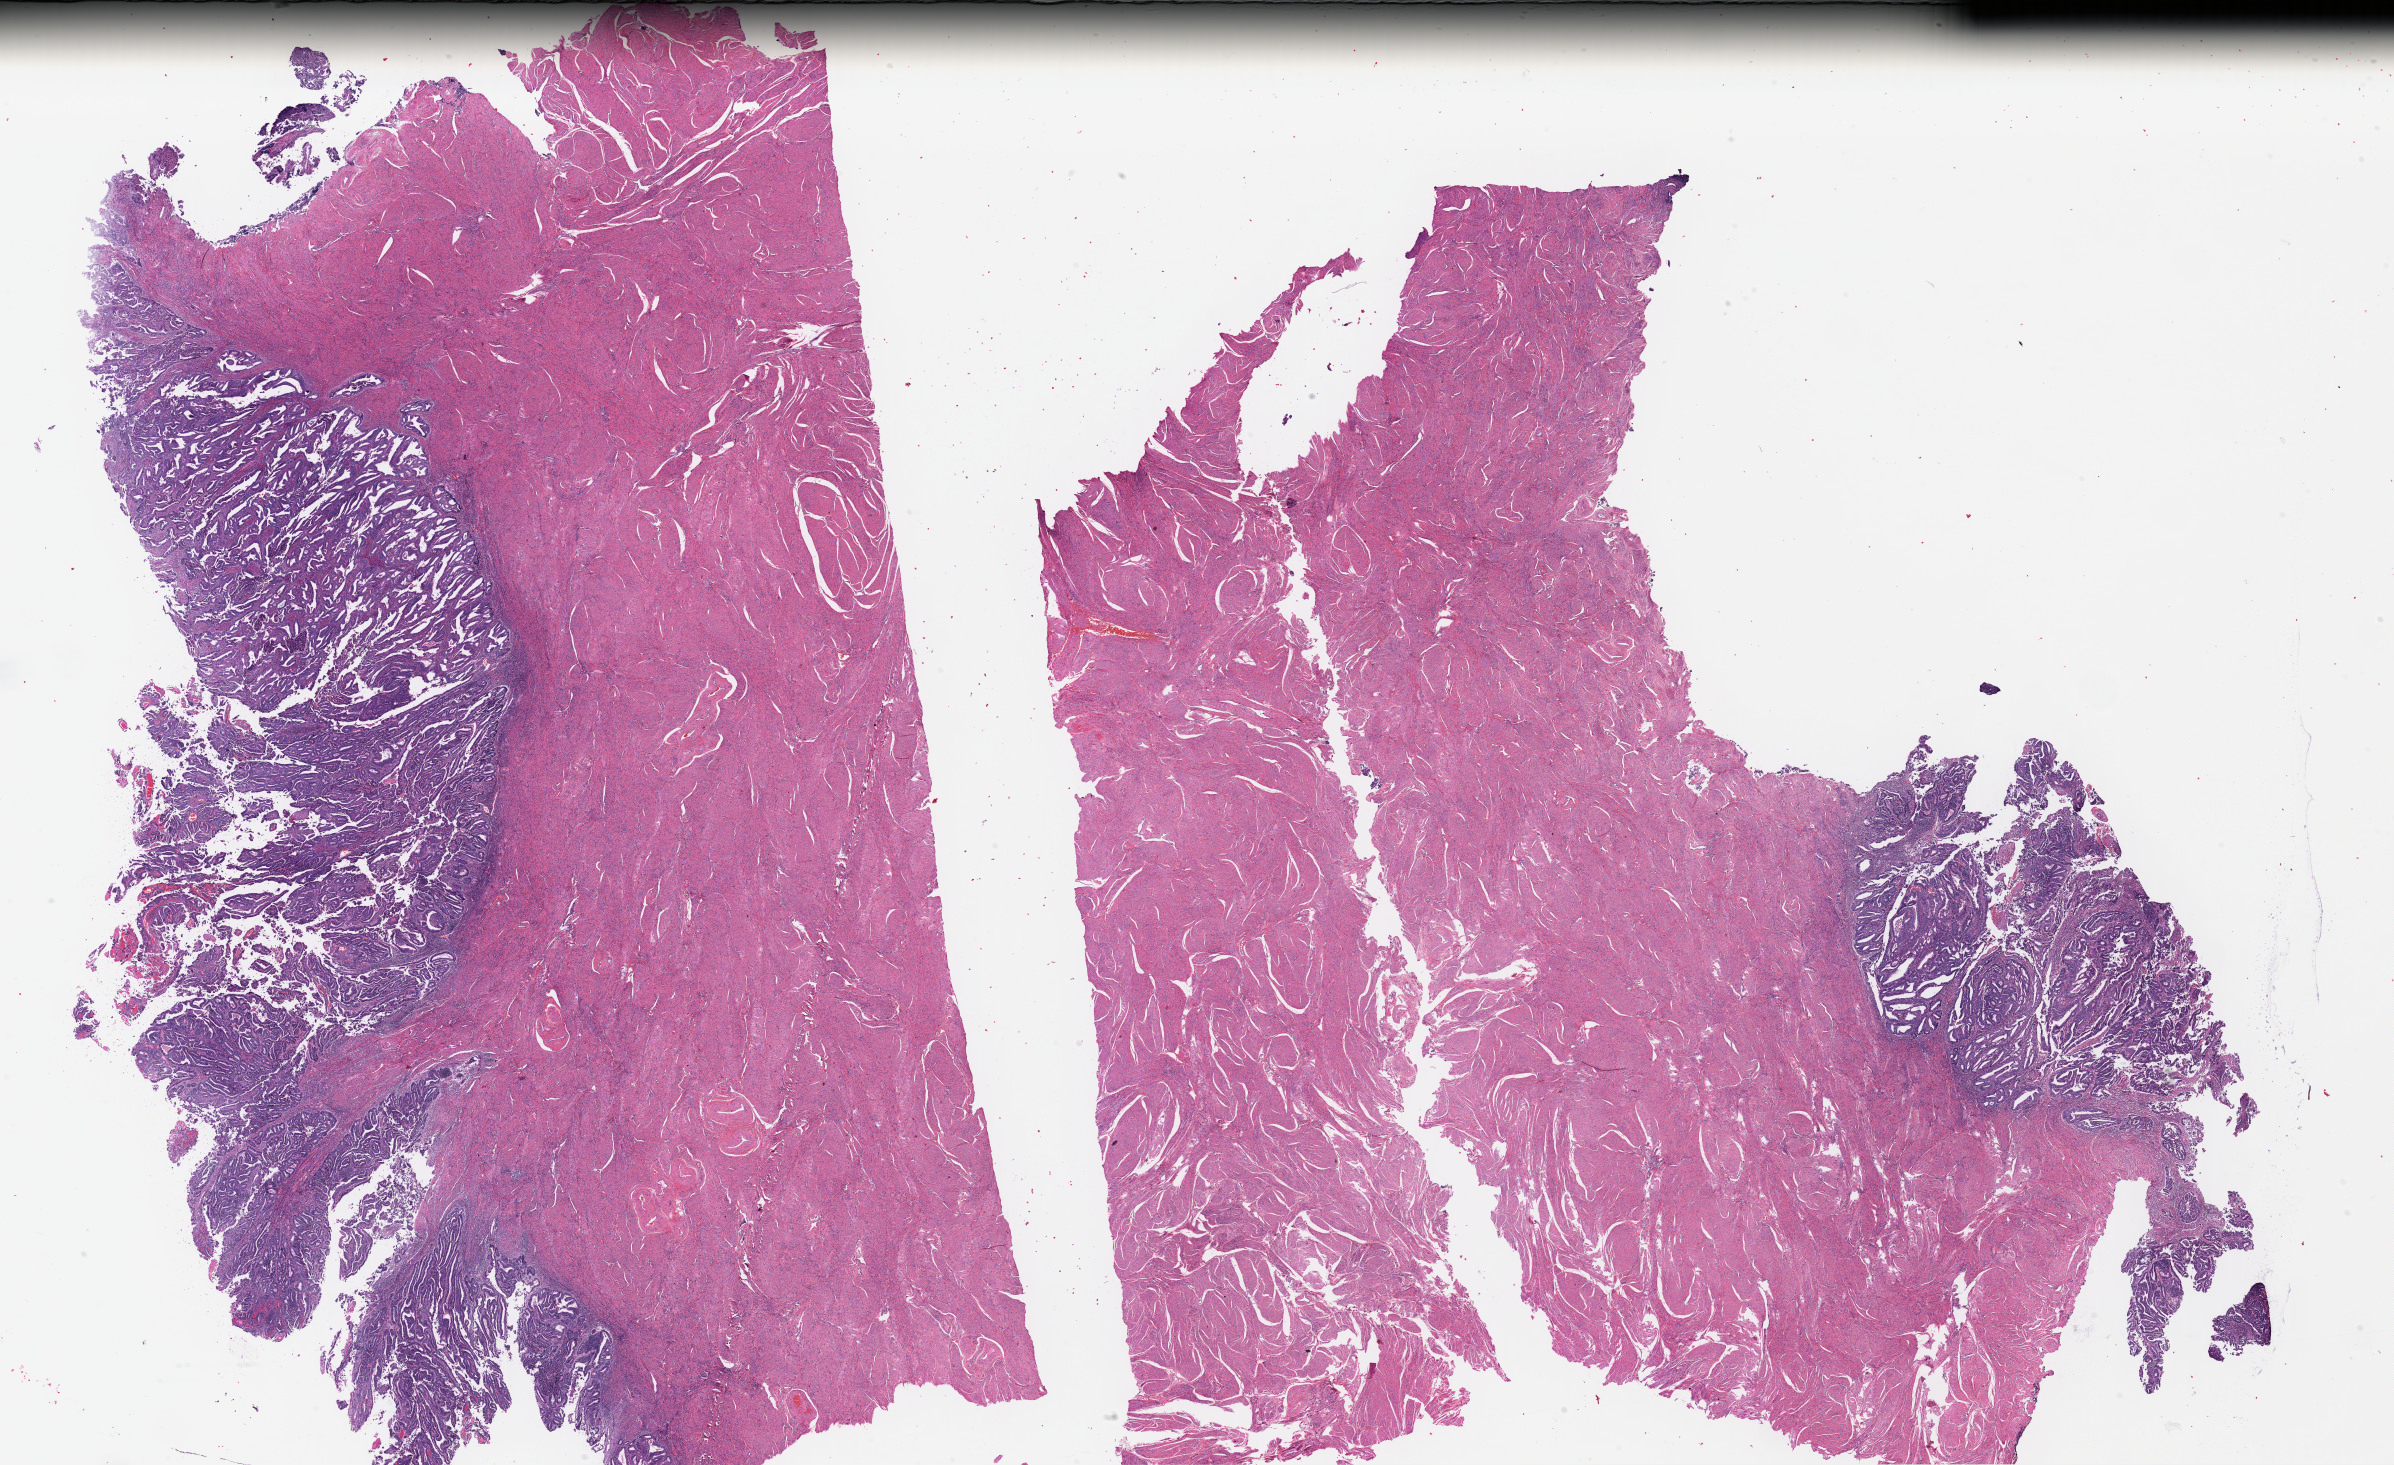
Digitized H&E tissue section (whole slide) — a low-resolution overview of the entire scanned area, about 37.6 x 23.0 mm; FFPE section; uterus, primary tumour sample. Patient: female, age at initial diagnosis 54 years. Histologic grade: G1 (well differentiated).
Diagnosis: Endometrioid adenocarcinoma, NOS (endometrium). Lymph nodes positive (case pathology): 0 of 32 examined. FIGO stage: IA.